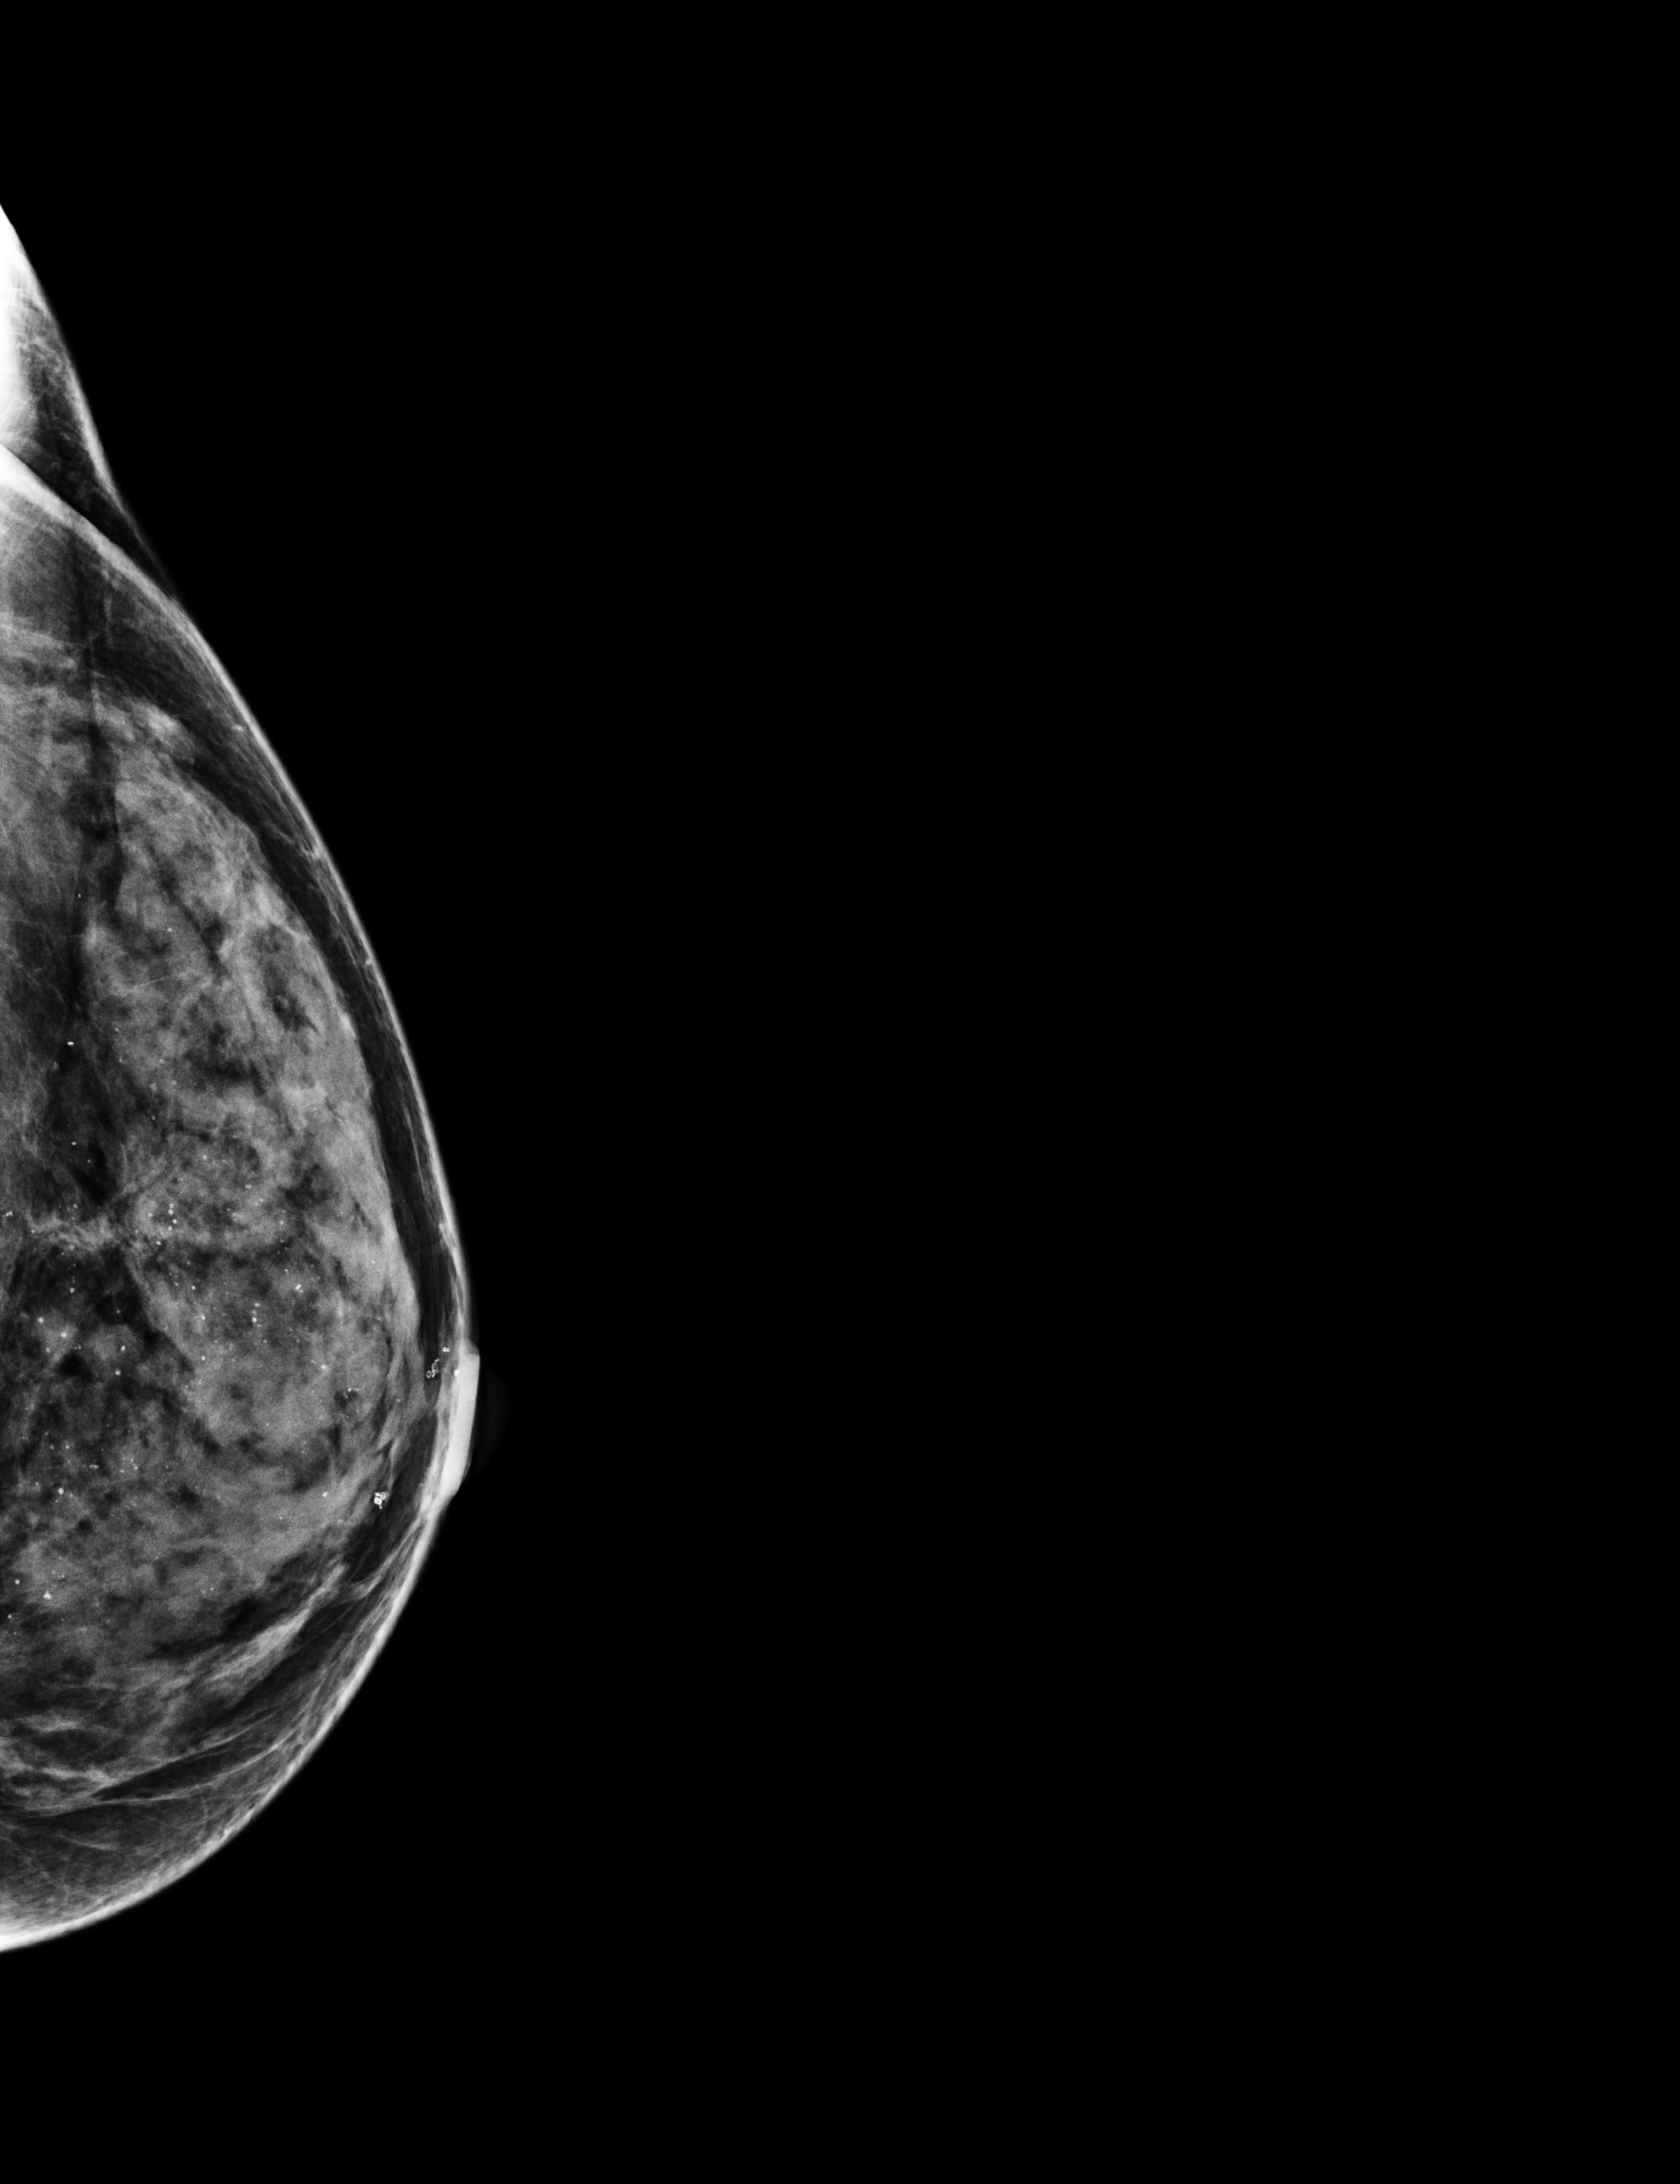
Full-field digital mammogram (FFDM); left breast; laterally exaggerated craniocaudal (XCCL) view; annual screening mammography examination; compressed breast thickness 40 mm. Patient: female, 49 years.
Breast density at the screening exam (both breasts): extremely dense (BI-RADS density category d). Final BI-RADS category for the screening round (tomosynthesis exam, both breasts): category 2. Recall: no recall after this screen.